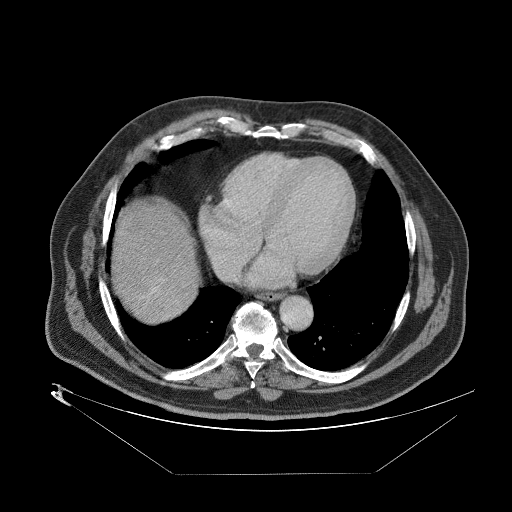
Contrast-enhanced abdominal CT (liver protocol), one axial slice. Slice 80 of 89 in the series (ordered by position). 140 kVp. One of 2 acquisitions stored at this slice position. Soft-tissue window (W 400 / L 40 HU). 512 × 512 image matrix, field of view 480 × 480 mm. Case-level facts recorded for this patient, not image findings: diagnosis: hepatocellular carcinoma (patient treated with transarterial chemoembolisation; whether this scan precedes or follows treatment is not stated here); TNM stage (as recorded): Stage-II; Child-Pugh class: B; tumour differentiation: moderately differentiated; tumour nodularity: multinodular.
Structures marked on this image (semi-automatically segmented with operator editing):
- abdominal aorta: bounding box [x1, y1, x2, y2] px = [276, 293, 311, 328]
- liver parenchyma outside the tumour (the mass and vessels are separate outlines, so this box may not span the whole liver): [112, 196, 192, 308]